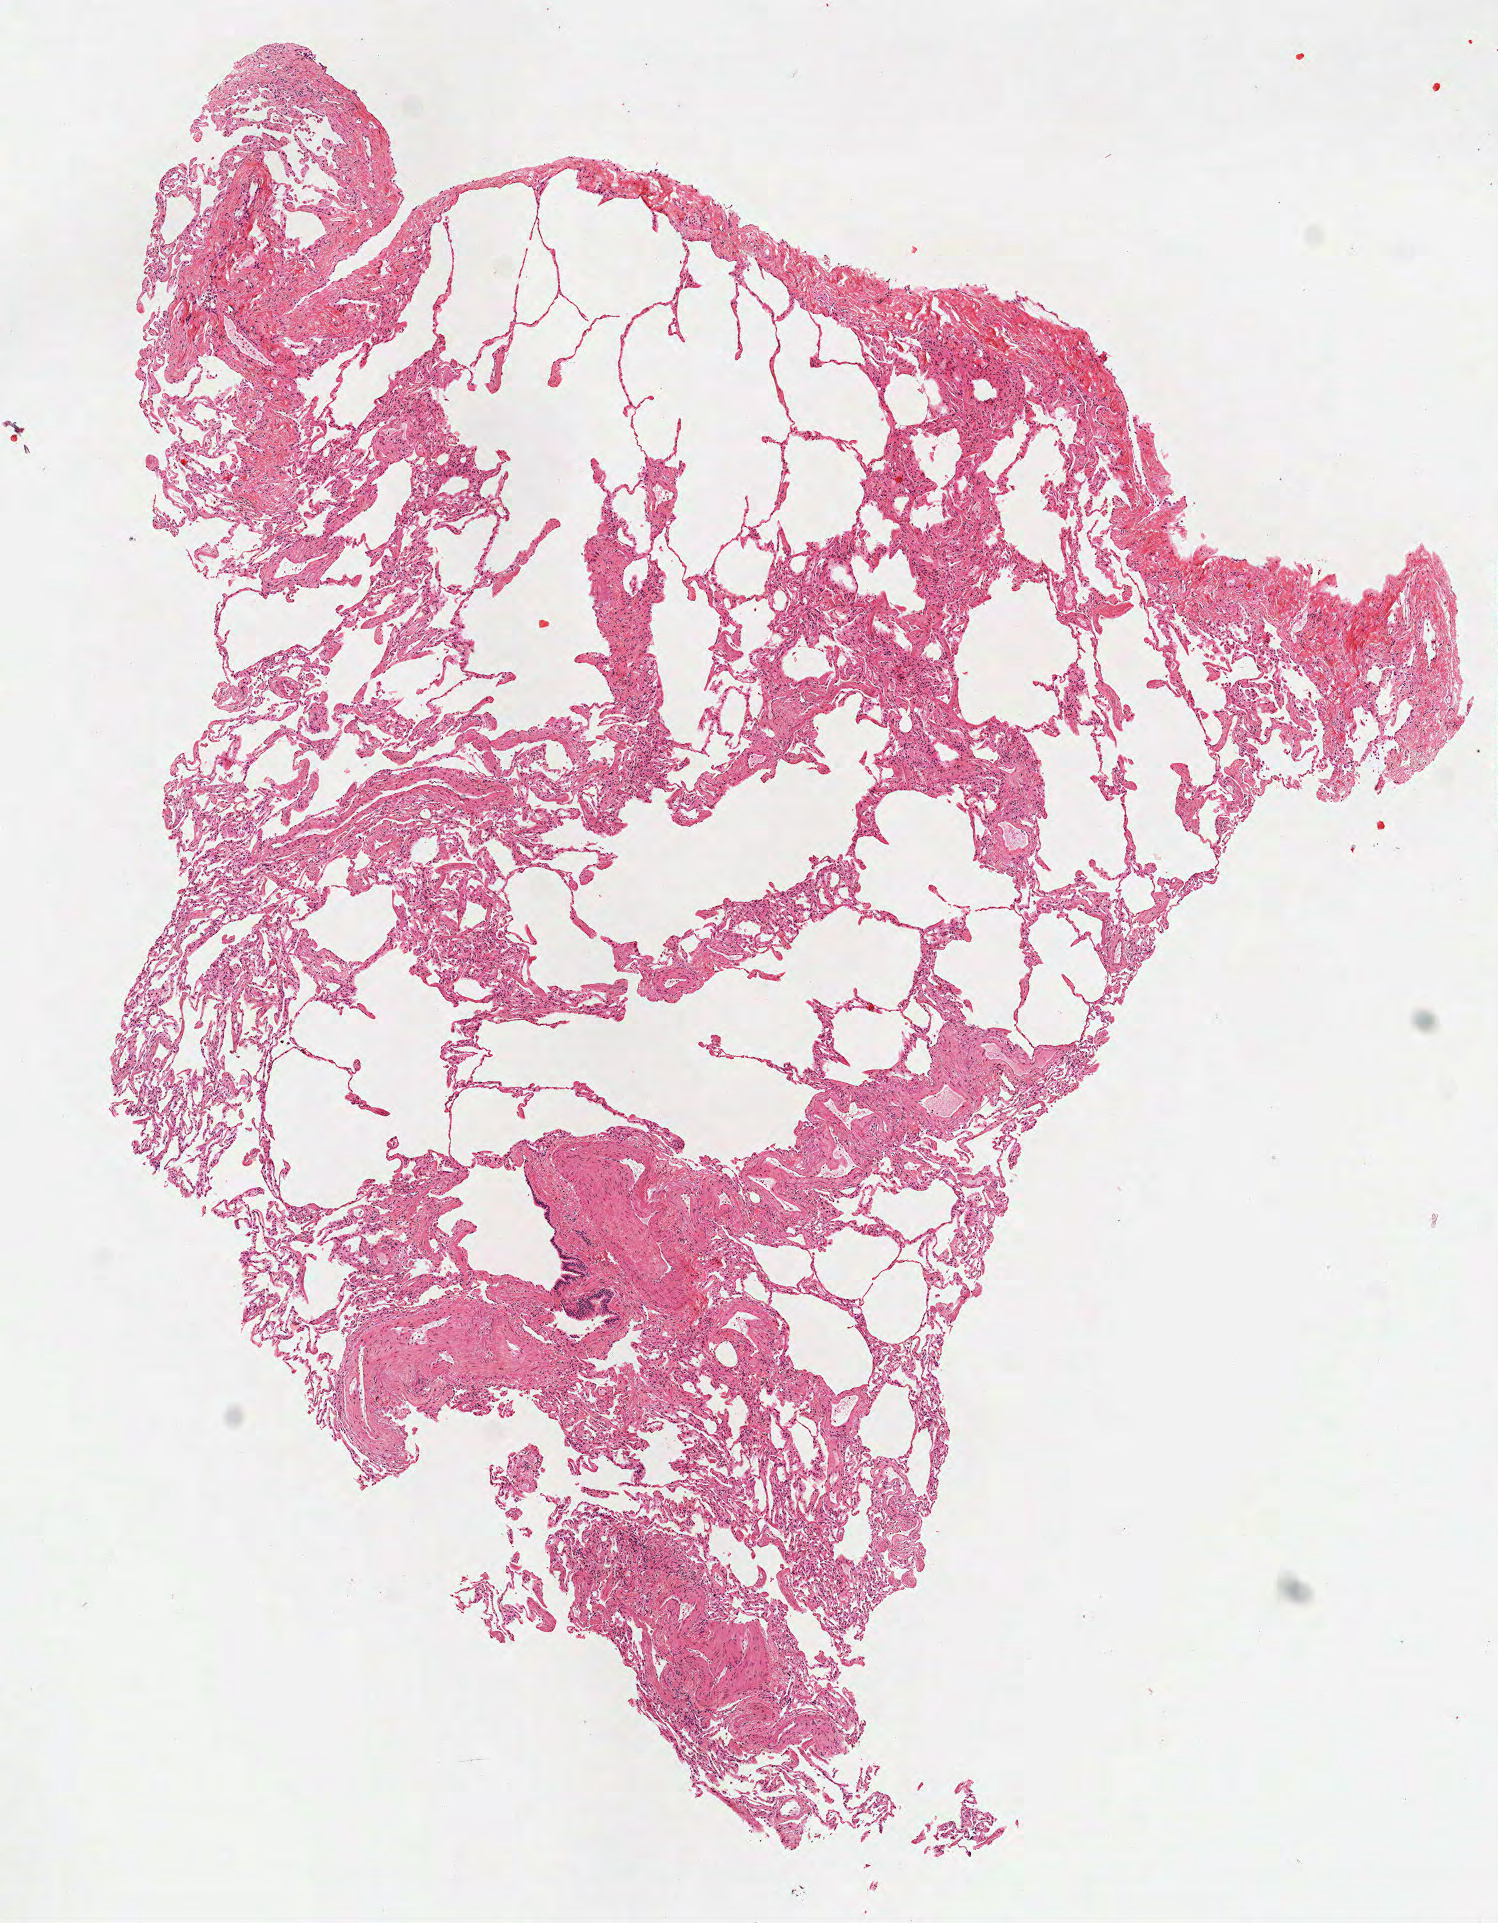
Whole-slide histology image, Hematoxylin and eosin (H&E) stained — whole scanned area (about 6.0 x 7.8 mm) shown as a low-resolution overview; frozen section; lung, solid tissue normal (non-tumour tissue) sample. Female patient; age at initial diagnosis 59 years.
This section: solid tissue normal sample (biorepository sample class). Patient diagnosis: Squamous cell carcinoma, NOS.